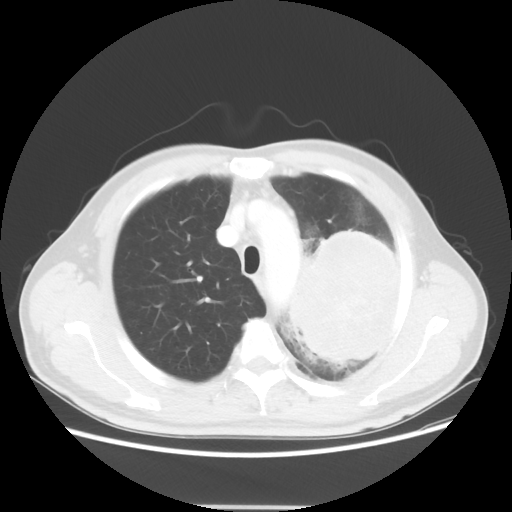
Chest CT, one axial slice; slice 42 of 53 in the series (ordered by position); reconstruction kernel STANDARD; 100 kVp; lung window (W 1500 / L -600 HU); 512 × 512 image matrix, field of view 391 × 391 mm. Male patient, age 60 years. Case-level facts recorded for this patient, not image findings: clinical TNM (as recorded): T4 N1 M1a; histopathological grade: G3.
Outlined on this slice (bounding box drawn by a radiologist):
- lung tumour (recorded histology: large cell carcinoma): bounding box [x1, y1, x2, y2] px = [287, 227, 416, 365]